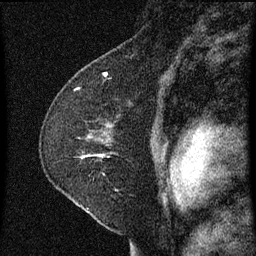
Breast MRI (dynamic contrast-enhanced), one sagittal slice. Position 44 of 60 along the scan axis. Dynamic contrast-enhanced series, image 2 of 3 at this slice position (ordered by acquisition). 1.5 T. TE 4.2 ms, TR 8 ms. 2 mm slice thickness. 256 × 256 image matrix, field of view 180 × 180 mm. Female patient, age 47 years.
Annotated regions visible in this slice (semi-automatic segmentation, software-assisted and operator-edited):
- analysis volume of interest (the breast-tissue region the enhancement analysis was run in; not a lesion): bounding box (x1, y1, x2, y2) in pixels: (49, 100, 158, 213)
- tumour enhancement mask (voxels above the 70 % enhancement threshold inside the analysis volume of interest): (82, 154, 104, 159)